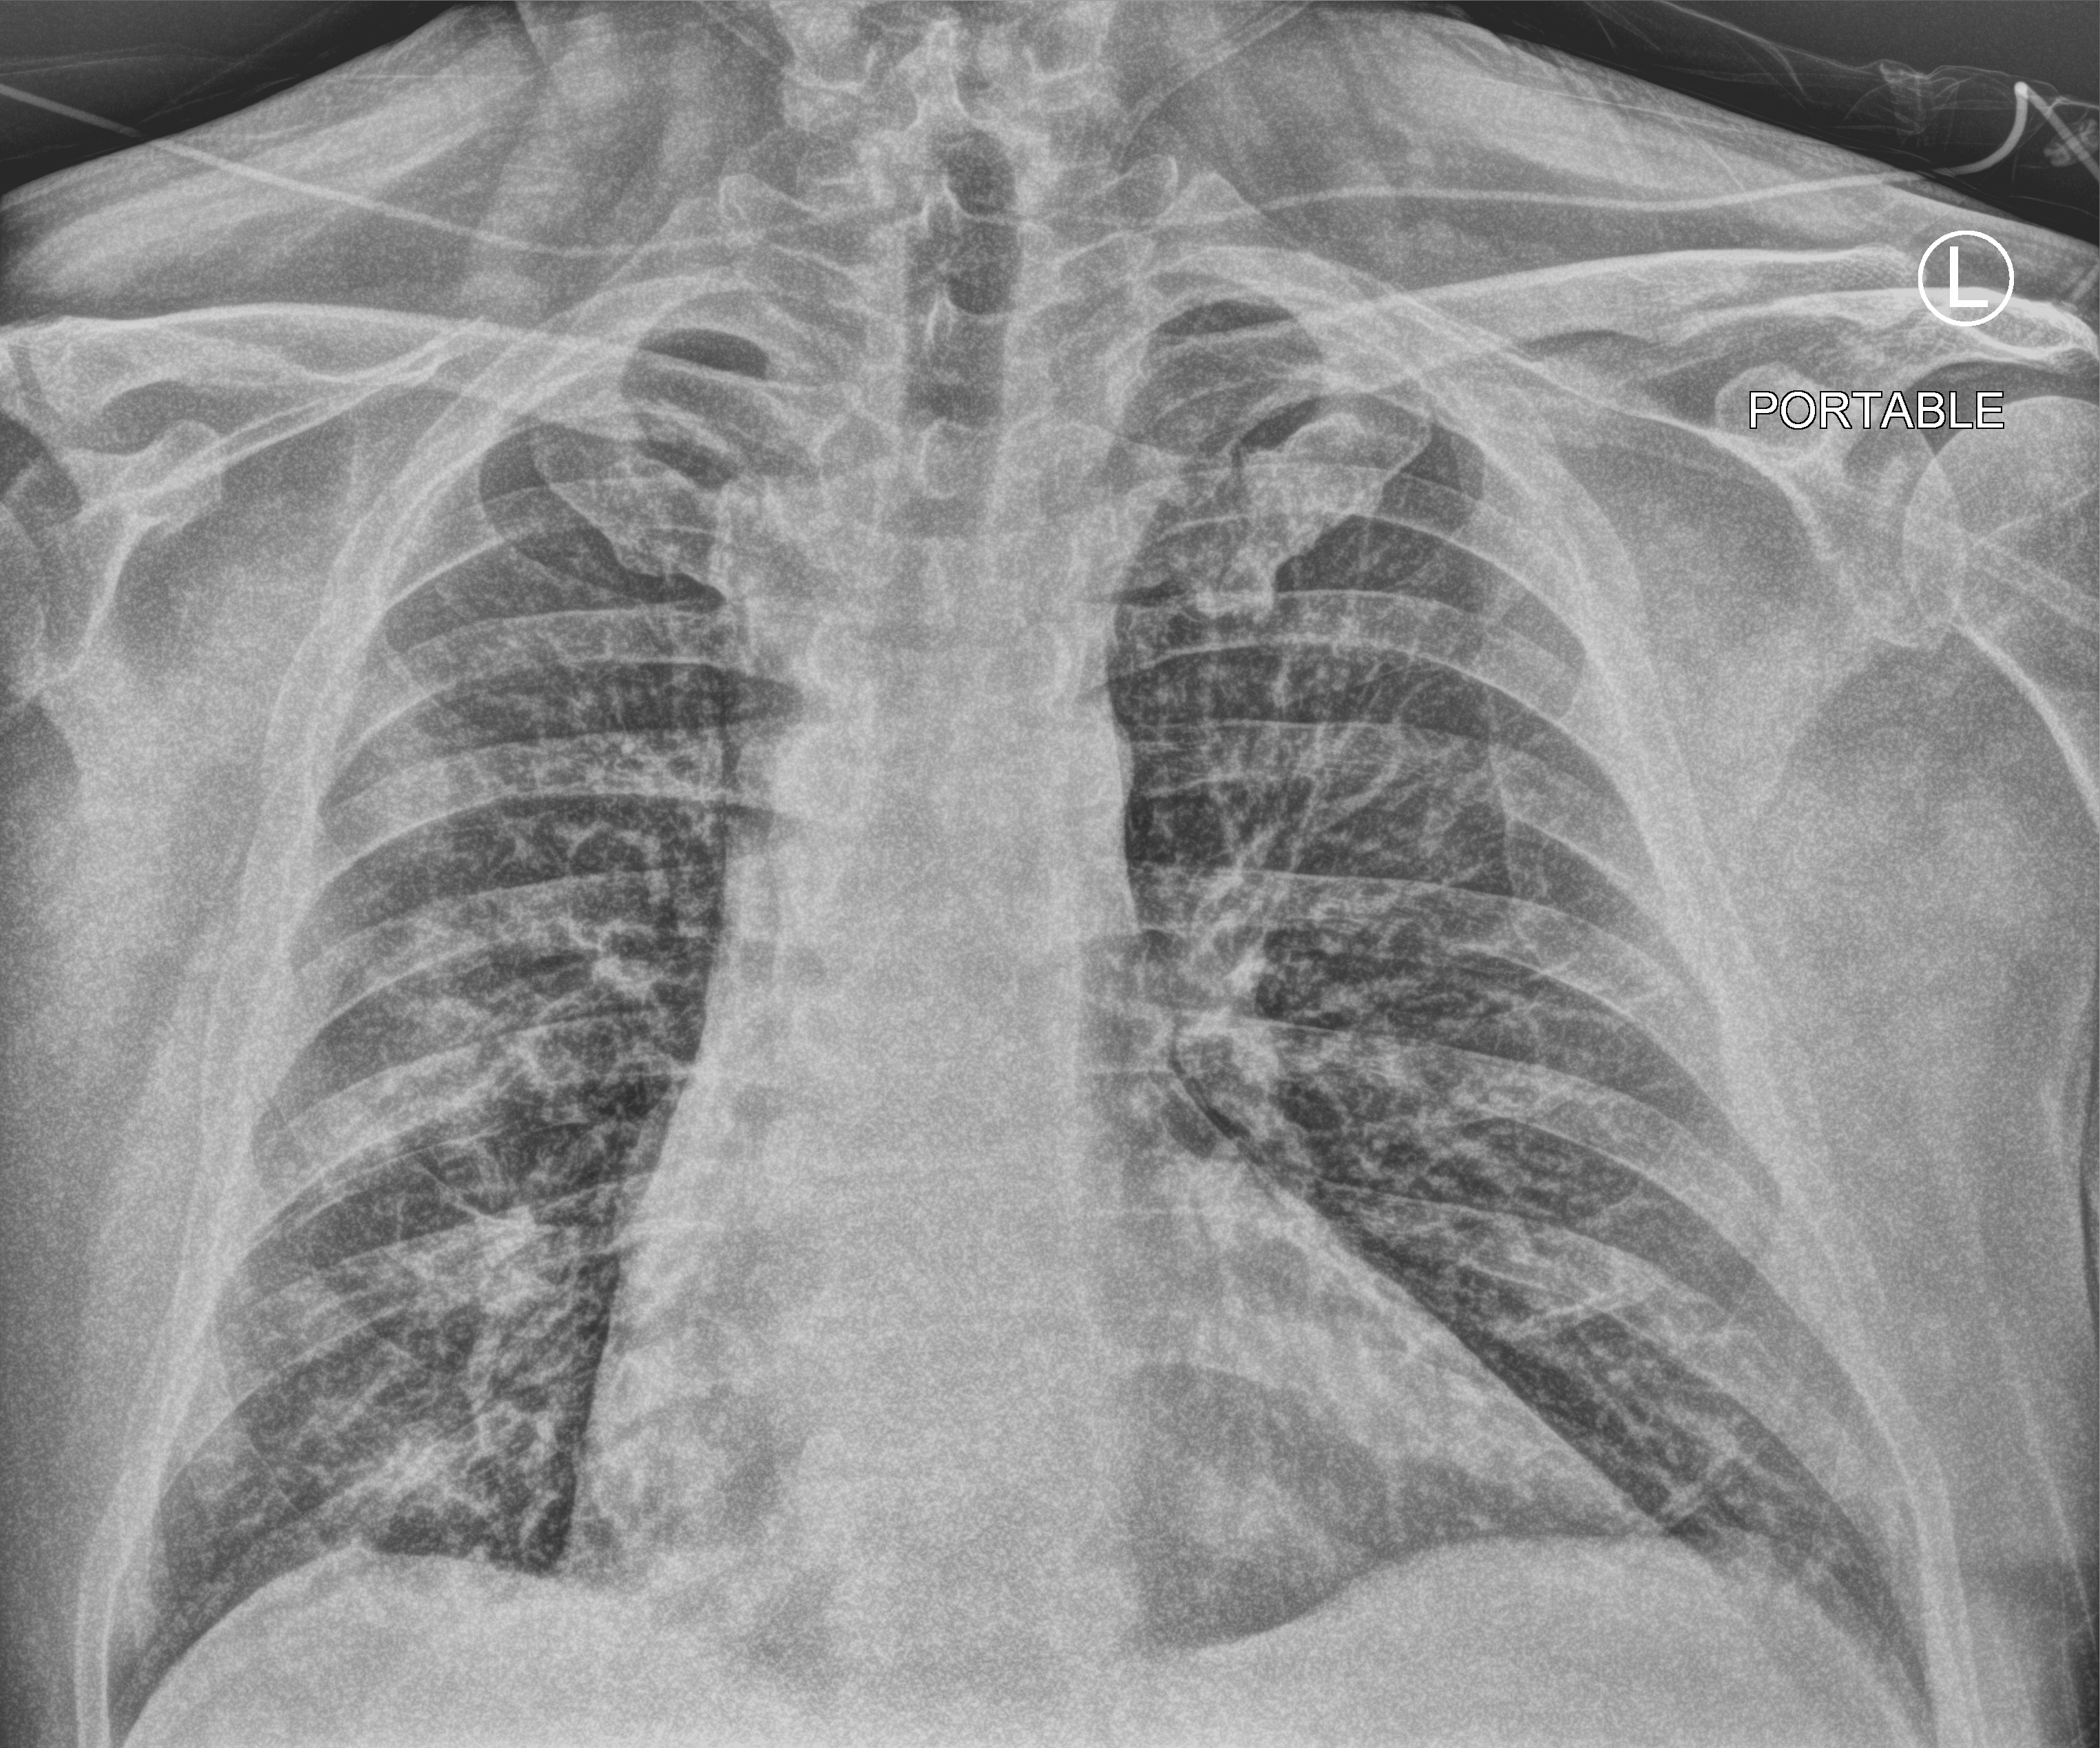
Portable chest radiograph; anteroposterior (AP) projection. Male patient hospitalised with COVID-19, age 18–59 years.
Admission-level facts for this patient (not findings on this image; timing relative to this image not recorded): mechanically ventilated during this hospital stay: no; admitted to intensive care during this hospital stay: no; length of hospital stay: 8 days.